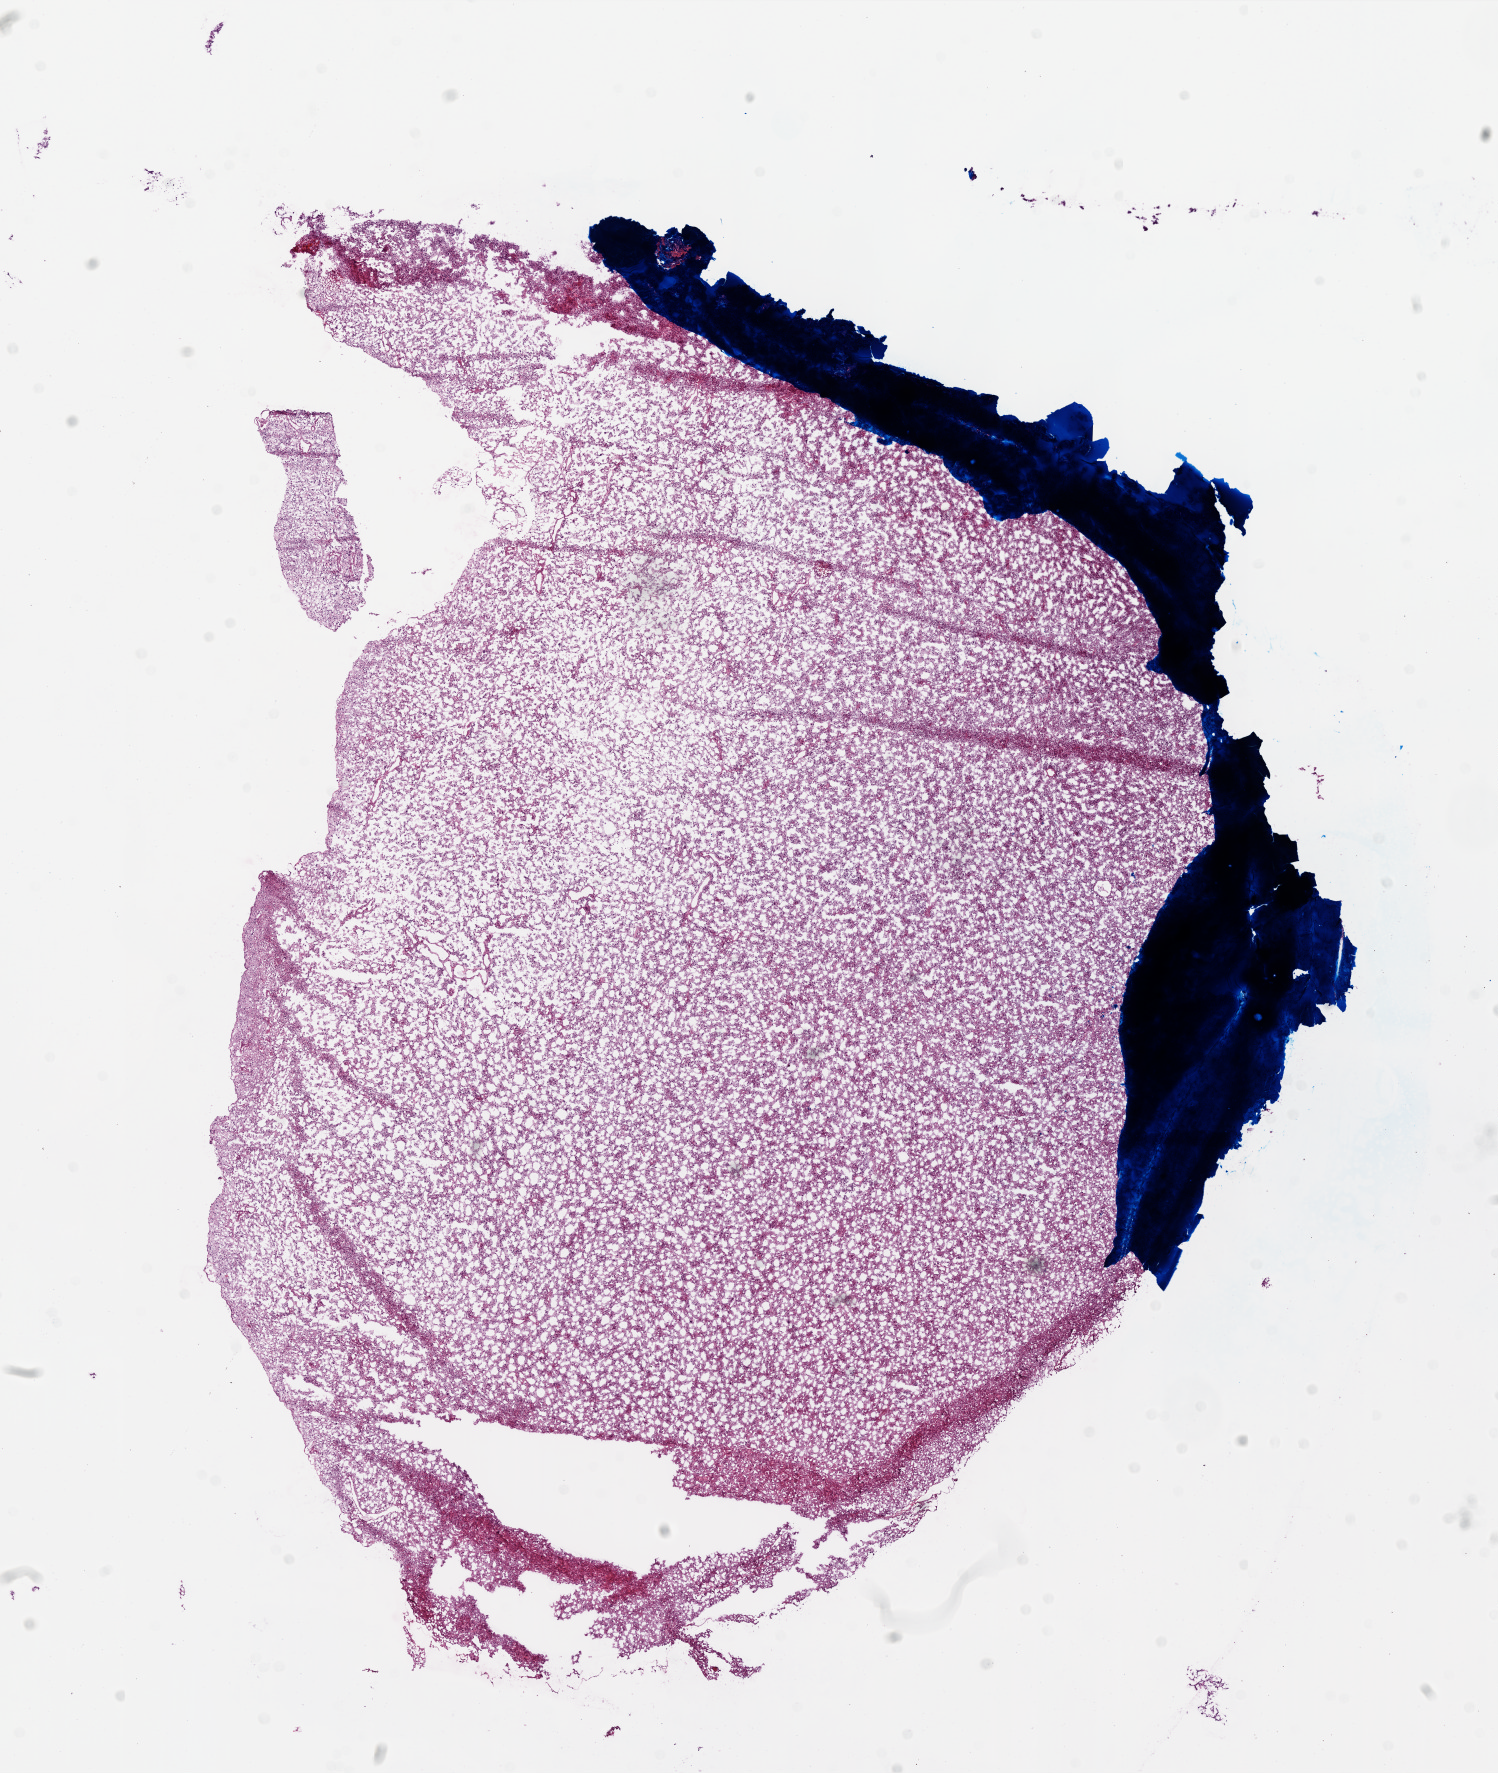
Whole-slide histology image, H&E, whole scanned area (about 12.0 x 14.2 mm, acquisition: 20x scan) shown as a low-resolution overview, frozen section, sample: primary tumour, brain. Patient: male, age at initial diagnosis 67 years. Composition of this section per pathologist review: tumour cells 100%, tumour nuclei 100%, normal cells 0%, stromal cells 0%, necrosis 0%. Inflammatory infiltration, as recorded: lymphocyte infiltration 0%.
* diagnosis: Glioblastoma